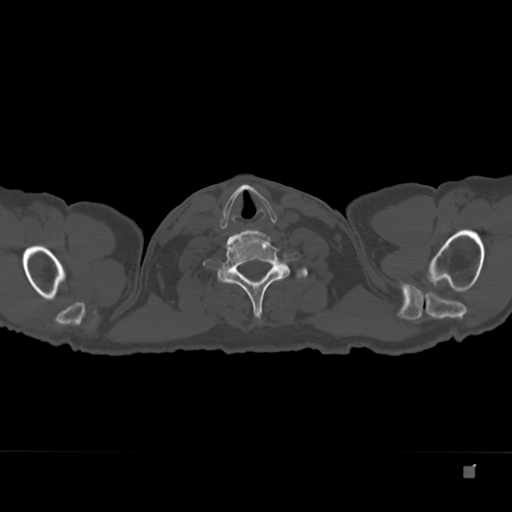
CT including the spine, one axial slice. Slice 327 of 332 in the series (ordered by position). 120 kVp. Bone window (W 1800 / L 400 HU). 1.5 mm slice thickness. 512 × 512 image matrix, field of view 389 × 389 mm. Male patient, age 72 years. From the clinical record (not read from this slice): primary cancer: skeletal.
Annotated regions visible in this slice (semi-automatically segmented with operator editing):
- T1 vertebra: box from (x=218, y=264) to (x=308, y=284) px